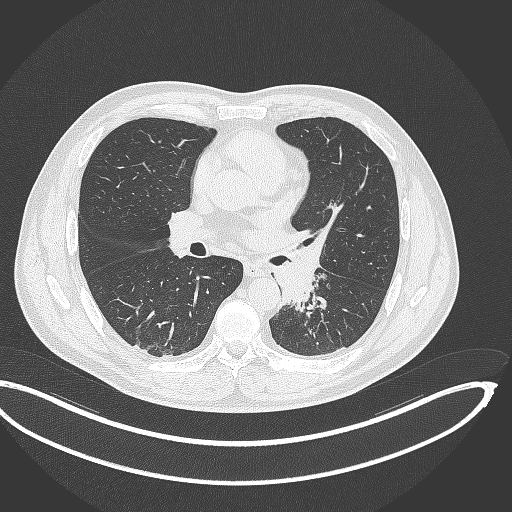
Chest CT, one axial slice; position 191 of 362 along the scan axis; 120 kVp; lung window (W 1500 / L -600 HU); 1 mm slice thickness; 512 × 512 image matrix, field of view 442 × 442 mm. Patient: male, 50 years. Case-level facts recorded for this patient, not image findings: clinical TNM (as recorded): T2a N3 M0.
Structures marked on this image (rectangle marked by the reading radiologist):
- lung tumour (recorded histology: squamous cell carcinoma): box from (x=269, y=239) to (x=325, y=307) px